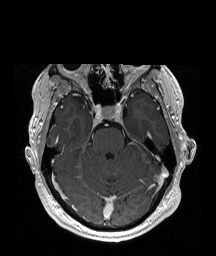
Brain MRI from a brain-tumour surgery series, one axial slice; position 130 of 192 along the scan axis; T1-weighted post-contrast; 1 mm slice thickness; 216 × 256 image matrix, field of view 219 × 260 mm. From the clinical record (not read from this slice): histopathology: Astrocytoma; WHO grade: 2; IDH mutation: yes; tumour location: Right Insular.
Outlined on this slice (outlined manually by an expert reader):
- tumour: bounding box <76,97,84,104> (left, top, right, bottom; pixels)